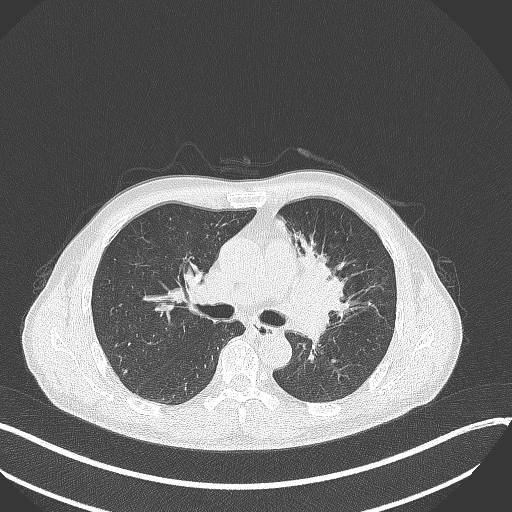
Chest CT, one axial slice; slice 203 of 411 in the series (ordered by position); lung window (W 1500 / L -600 HU); 1 mm slice thickness; 512 × 512 image matrix, field of view 400 × 400 mm. Patient: male, 56 years. Case-level facts recorded for this patient, not image findings: clinical TNM (as recorded): T2a N0 M0.
Structures marked on this image (bounding box drawn by a radiologist):
- lung tumour (recorded histology: squamous cell carcinoma): bounding box (x1, y1, x2, y2) in pixels: (285, 246, 360, 327)